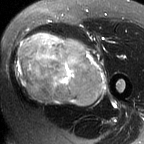
MRI of an extremity soft-tissue mass, one axial slice; slice 32 of 60 in the series (ordered by position); T2-weighted fat-saturated; MR volume resampled by the dataset authors to the PET/CT grid (not the native acquisition matrix); 3.27 mm slice thickness; 144 × 144 image matrix. Female patient. From the clinical record (not read from this slice): histological type: pleiomorphic leiomyosarcoma; grade: intermediate; site of the primary tumour: left thigh.
Structures marked on this image (expert contour drawn on MRI and transferred to this co-registered scan by the dataset authors):
- gross tumour volume including surrounding oedema: bounding box <15,33,106,107> (left, top, right, bottom; pixels)
- gross tumour volume (mass): <15,33,103,105>